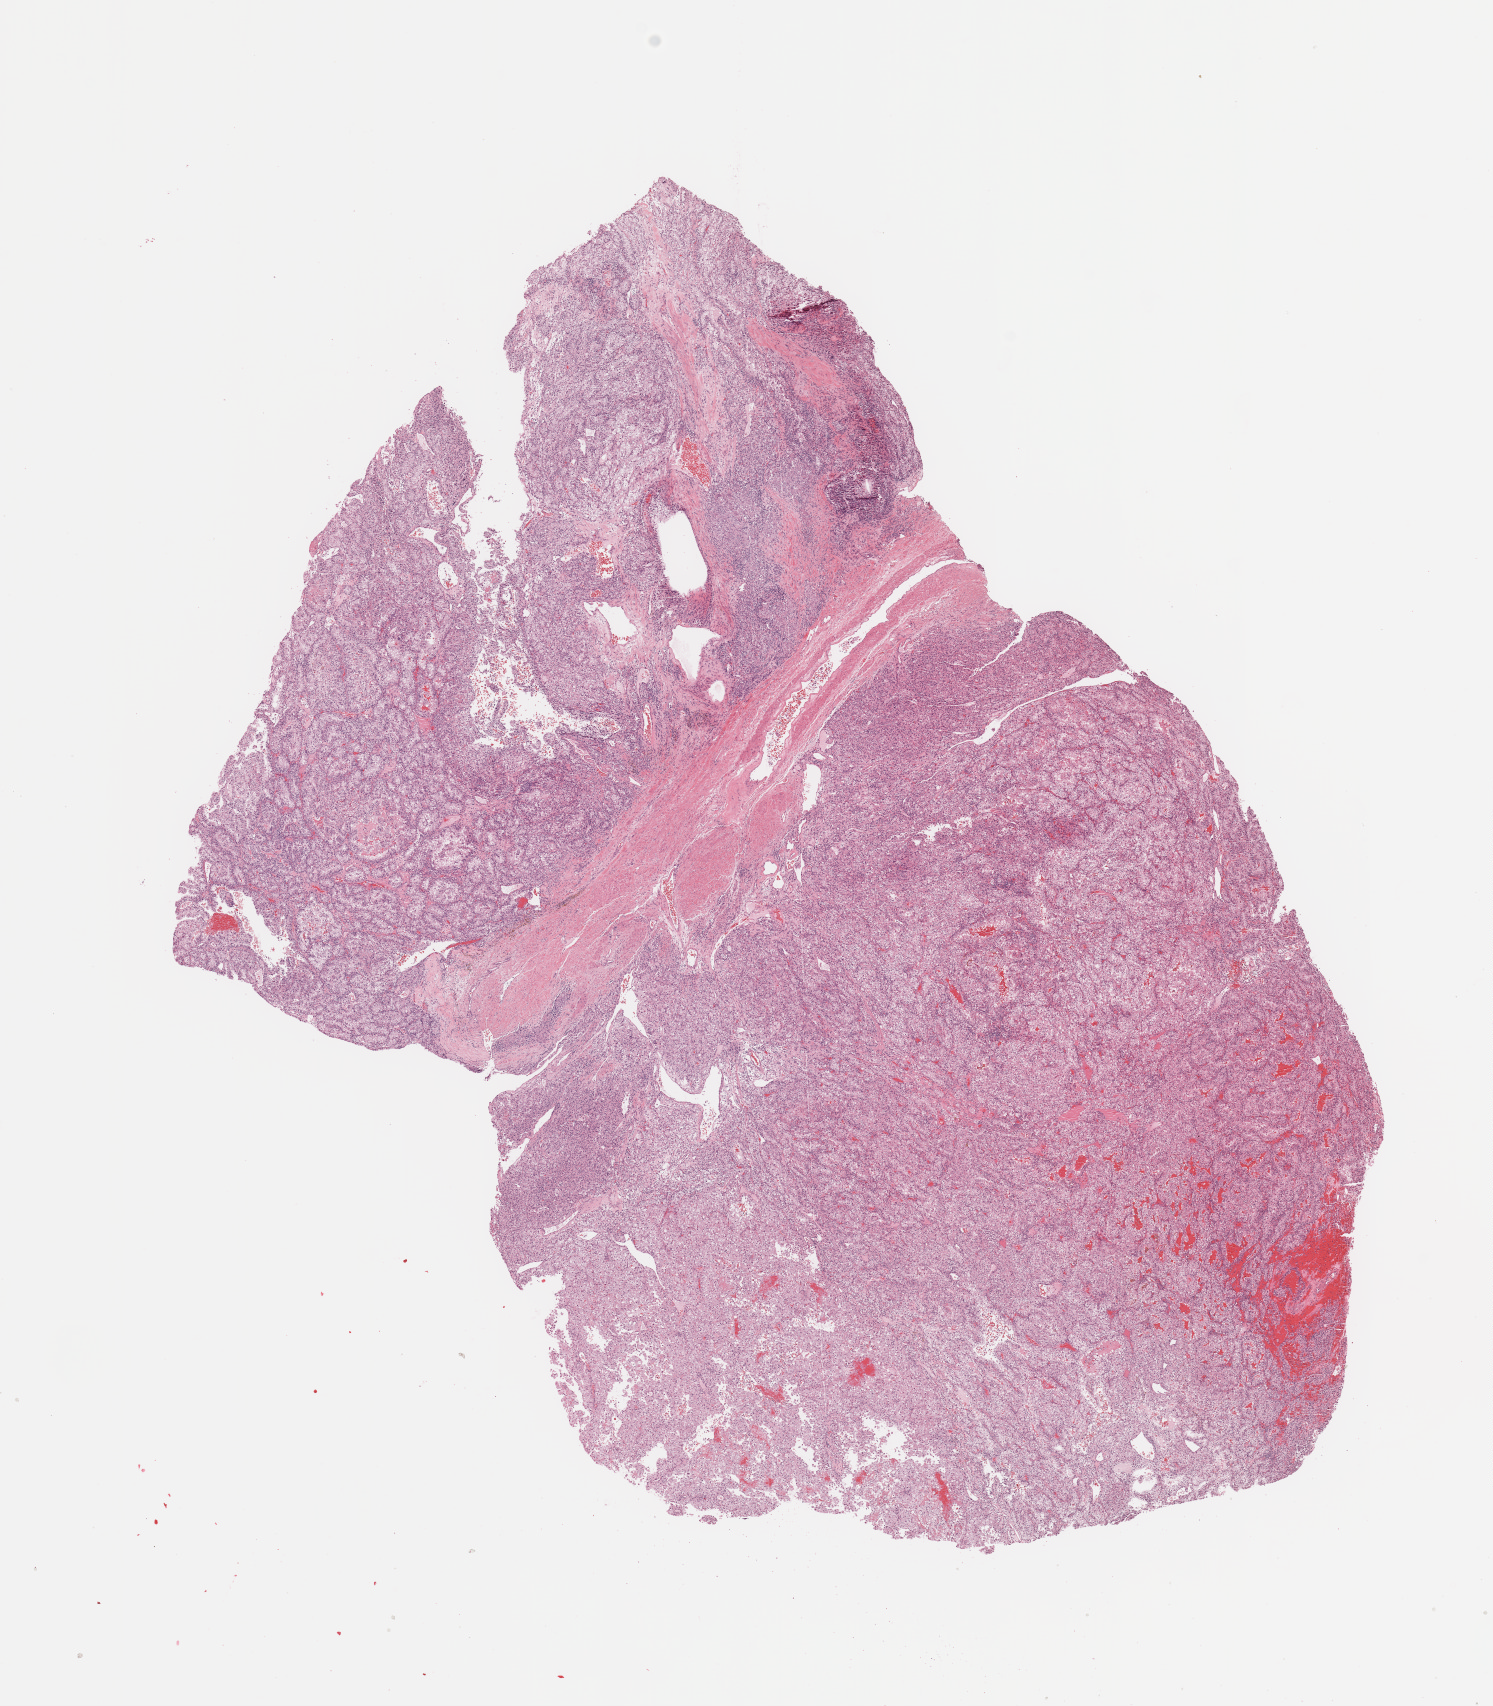
Digitized H&E tissue section (whole slide) — shown as a low-resolution overview of the whole scanned area (about 11.8 x 13.5 mm, slide scanned at 20x). Tumour tissue sample, sampled site: kidney. 60-year-old male patient. Histologic grade: G4 (undifferentiated). Pathologist review of this section (percent, as recorded): tumour nuclei 85%, necrosis 5%.
Histologic diagnosis: Renal cell carcinoma, NOS. AJCC pathologic stage: III.